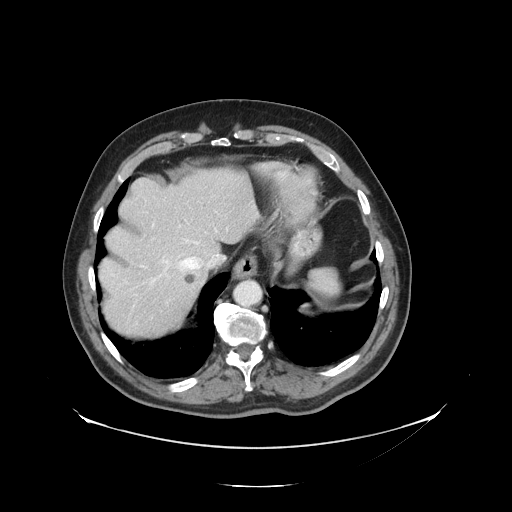
Contrast-enhanced abdominal CT, one axial slice. Slice 112 of 138 in the series (ordered by position). 120 kVp. Soft-tissue window (W 400 / L 40 HU). 512 × 512 image matrix, field of view 497 × 497 mm. Male patient, age 77 years. Case-level facts recorded for this patient, not image findings: diagnosis: colorectal cancer liver metastases, imaged before liver resection; multiple liver metastases: no; largest metastasis: 1.5 cm; disease in both lobes: no.
Structures marked on this image (outlined manually by an expert reader):
- hepatic veins: bounding box (x1, y1, x2, y2) in pixels: (140, 211, 218, 287)
- liver: (100, 169, 255, 337)
- planned liver remnant (the part of the liver to remain after resection): (100, 169, 256, 290)
- portal vein (with intrahepatic branches): (166, 196, 214, 303)
- liver metastasis: (184, 274, 197, 285)